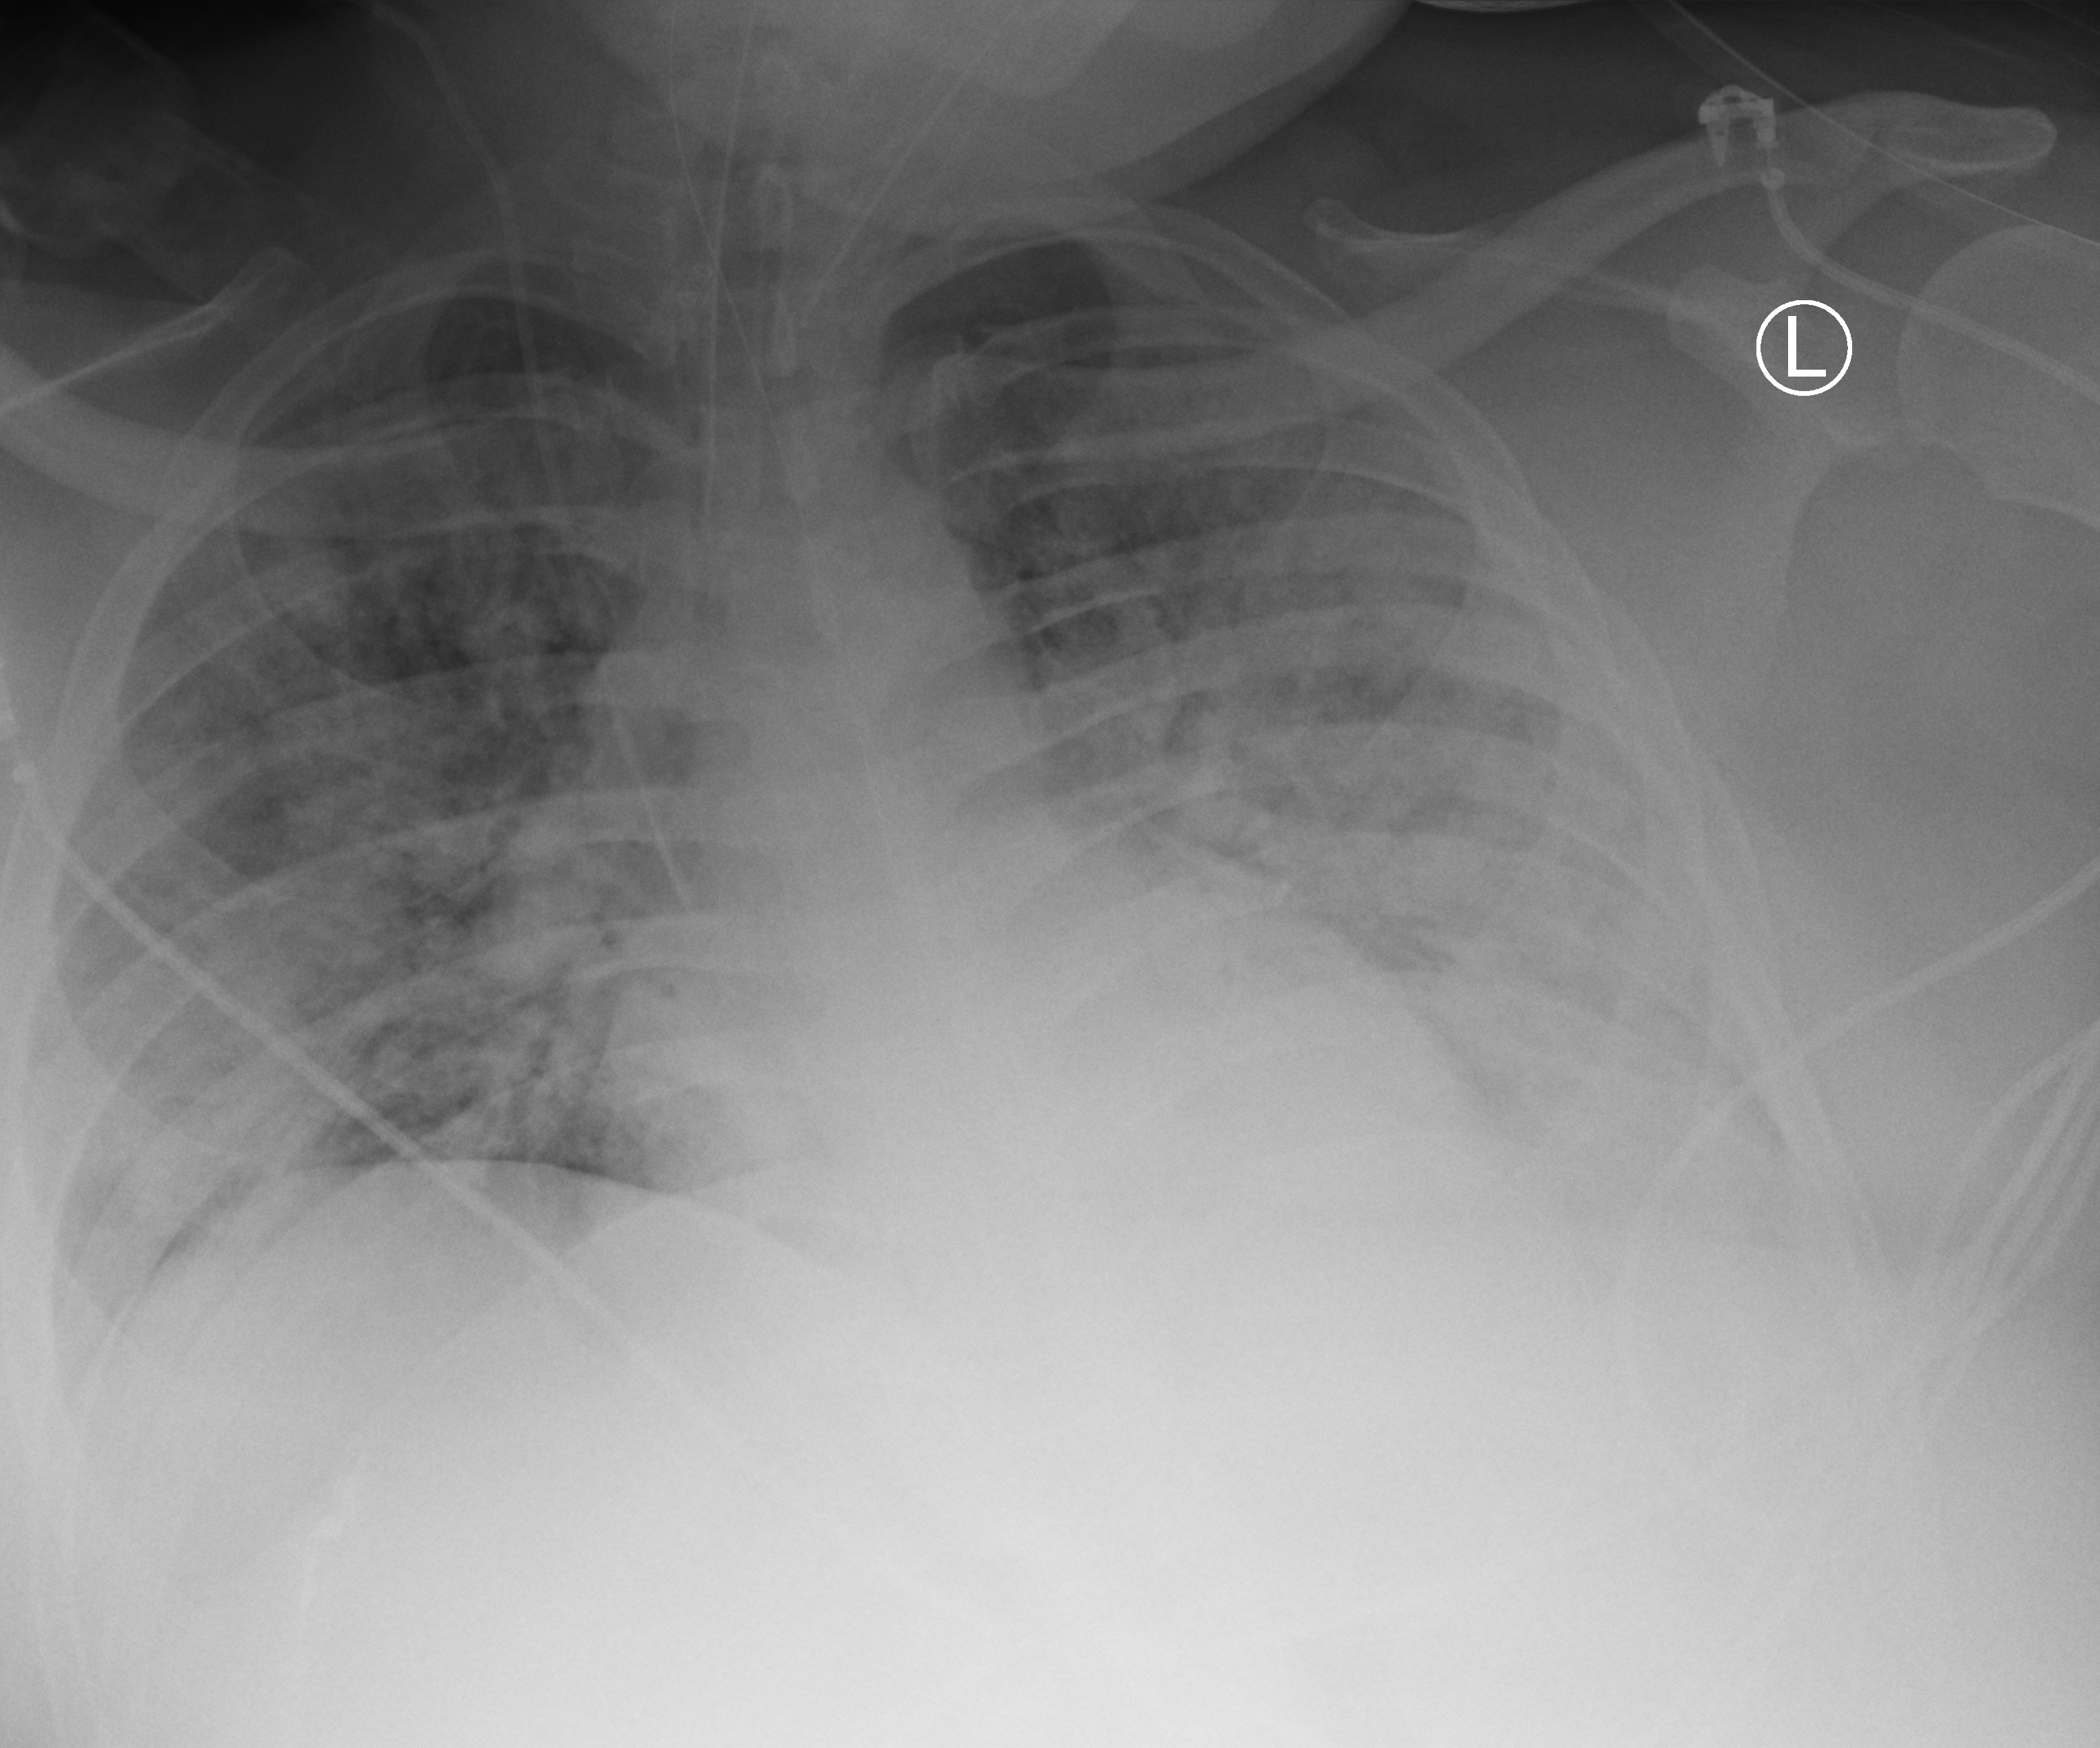
Bedside chest radiograph (computed radiography). Male patient hospitalised with COVID-19, age 18–59 years.
From the hospital-stay record, not from the radiograph (when in the stay this image was taken is not recorded): mechanically ventilated during this hospital stay: yes; admitted to intensive care during this hospital stay: yes; chronic kidney disease (admission record): no.